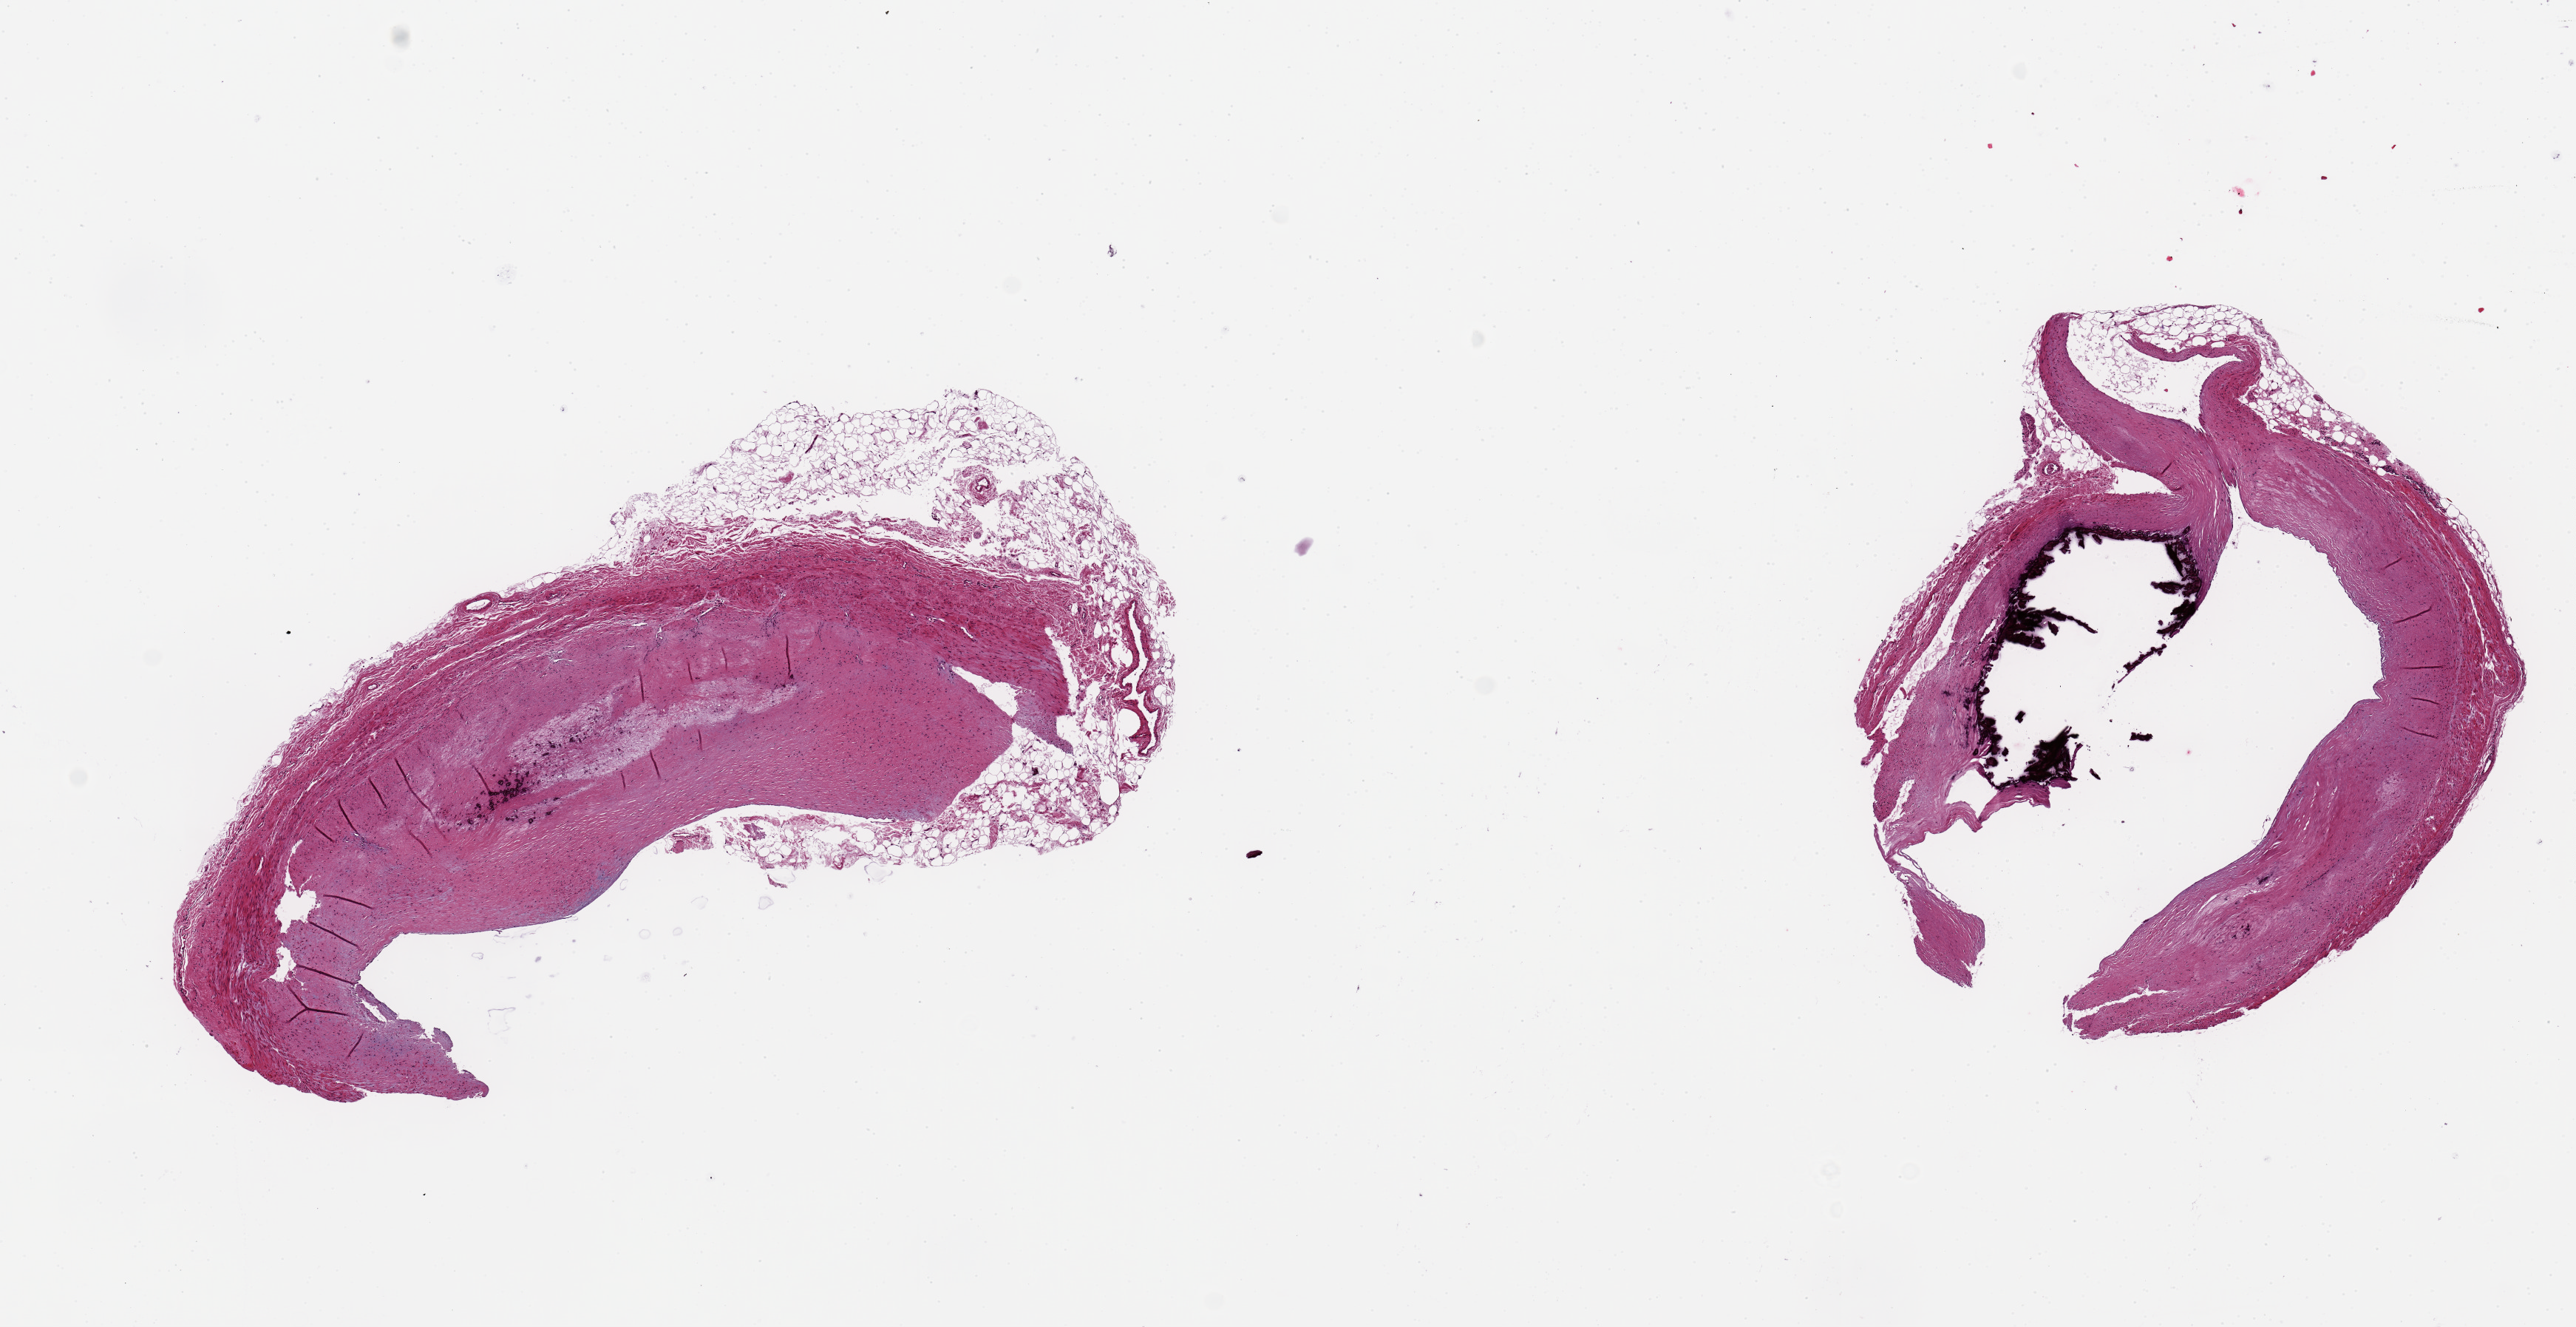
Digitized H&E-stained section — low-resolution overview of the scanned area, about 13.8 x 7.1 mm (from a 20x scan); PAXgene-fixed, paraffin-embedded tissue; target tissue: coronary artery; tissue donor sample. Male donor.
Pathologist's review note for this sample: 2 ~3x2mm aliquots, 30% occlusive calcified atherosis in one.